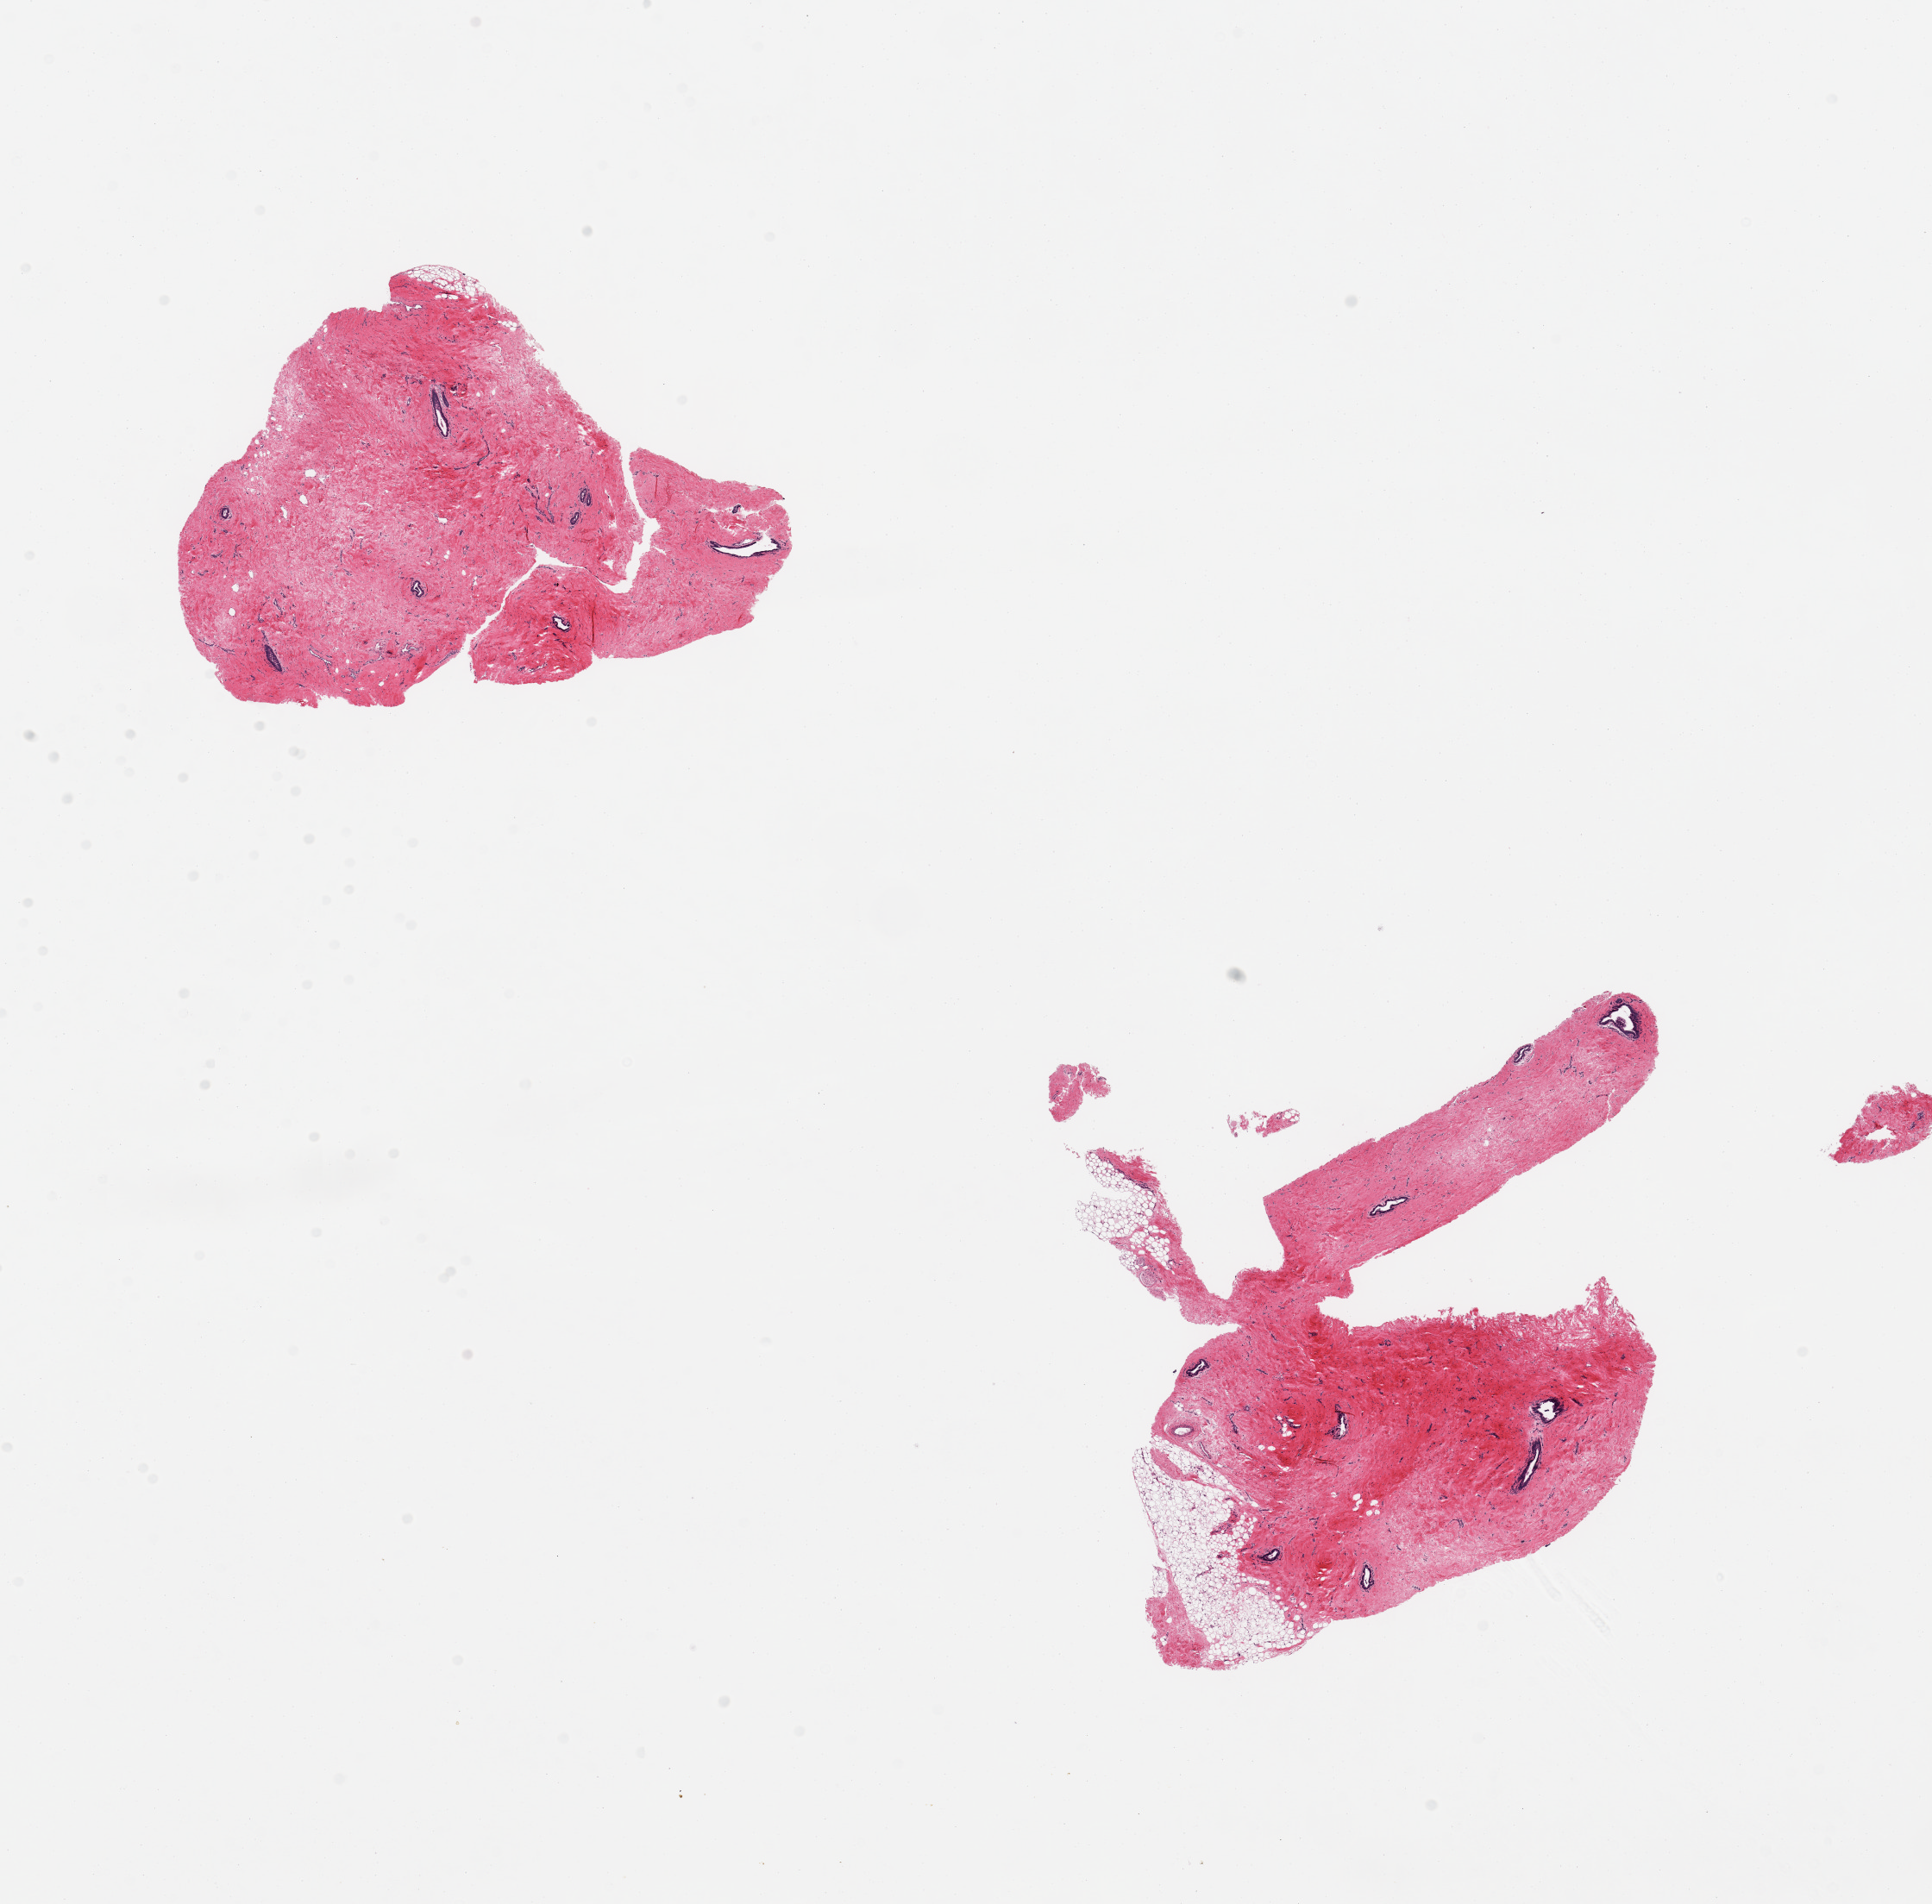
Whole-slide image, haematoxylin and eosin stain — shown as a low-resolution overview of the whole scanned area (about 17.7 x 17.5 mm), PAXgene-fixed paraffin-embedded (PFPE) section, sampled site (target tissue): breast, donor tissue sample. Male donor.
Pathologist's review note for this sample: 2 pieces, gynecomastoid stromal hyerplasia, ductal elements present.